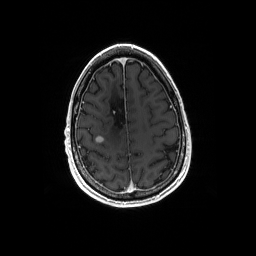
Brain MRI from a brain-tumour surgery series, one axial slice; T1-weighted post-contrast; 1 mm slice thickness; 256 × 256 image matrix, field of view 256 × 256 mm. From the clinical record (not read from this slice): histopathology: Astrocytoma; WHO grade: 4; IDH mutation: yes.
Structures marked on this image (outlined manually by an expert reader):
- tumour: box from (x=95, y=137) to (x=104, y=144) px